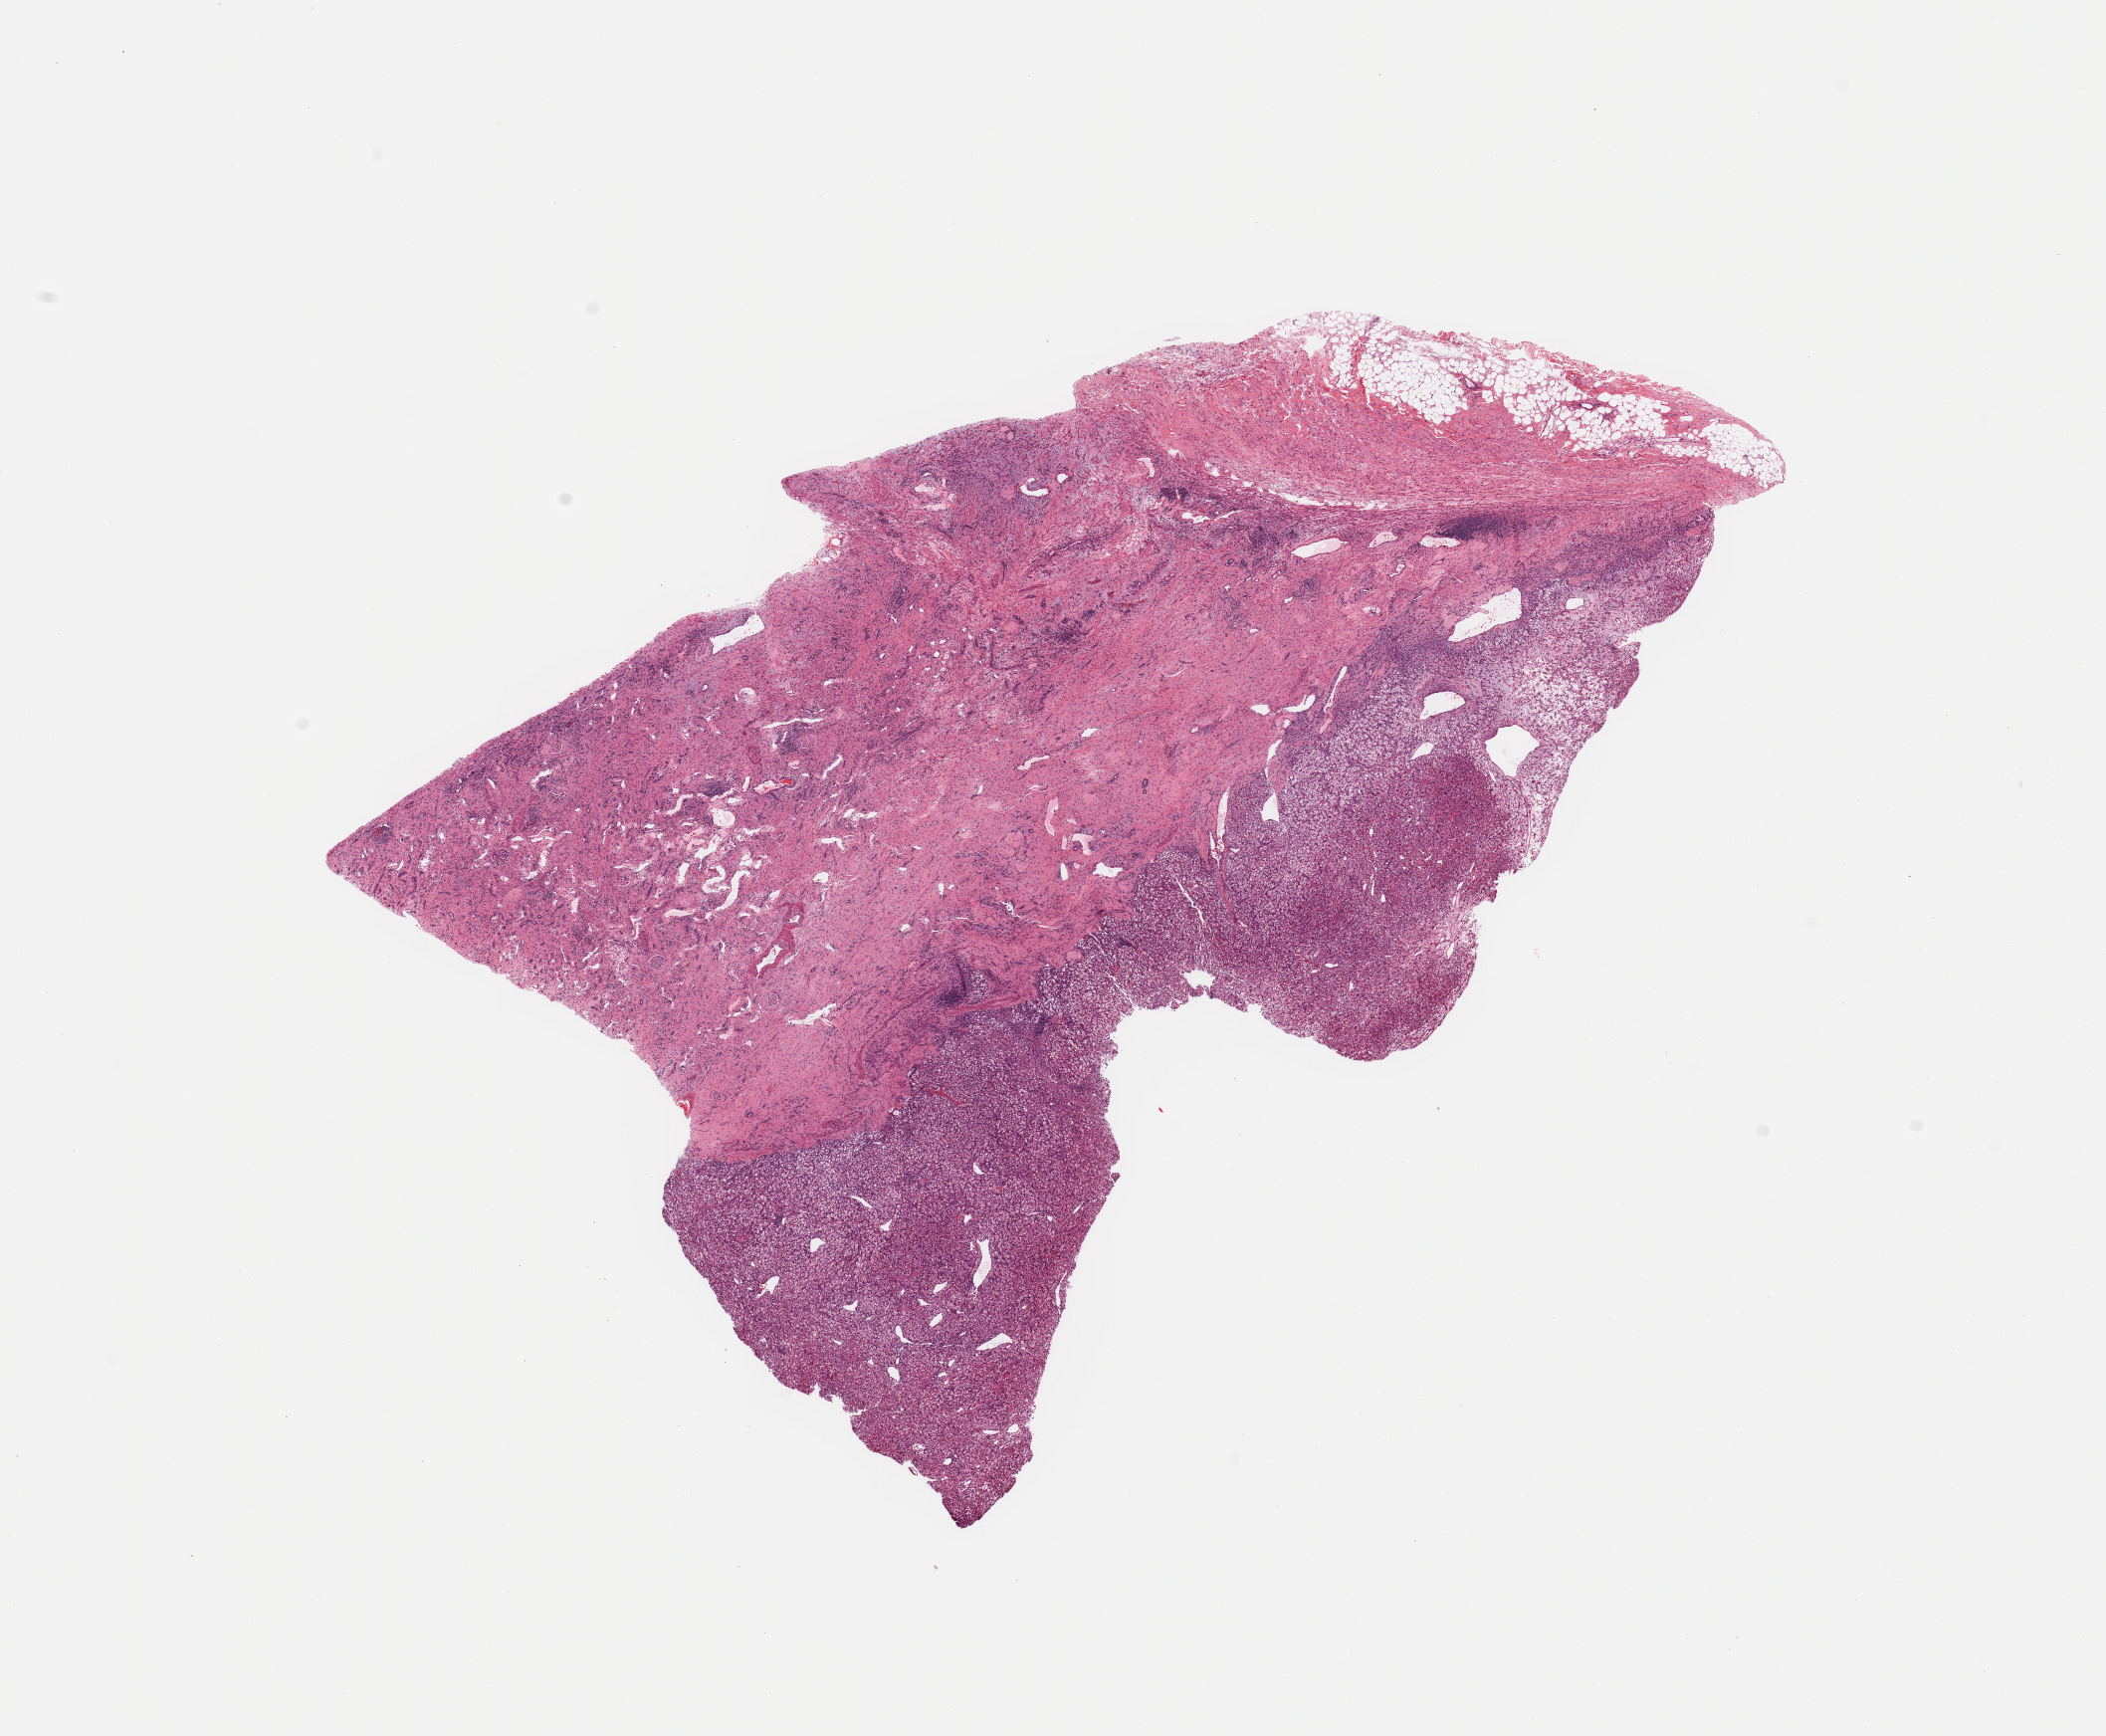
H&E whole-slide image — whole scanned area (about 16.7 x 13.8 mm) shown as a low-resolution overview; tumour tissue sample, sampled site: kidney. Male, 47 y/o. Histologic grade: G3 (poorly differentiated). Slide review estimates, as recorded: tumour nuclei 60%, necrosis 5%.
Primary tumour site (as recorded): upper pole. AJCC pathologic stage: I. Diagnosis: Renal cell carcinoma, NOS.